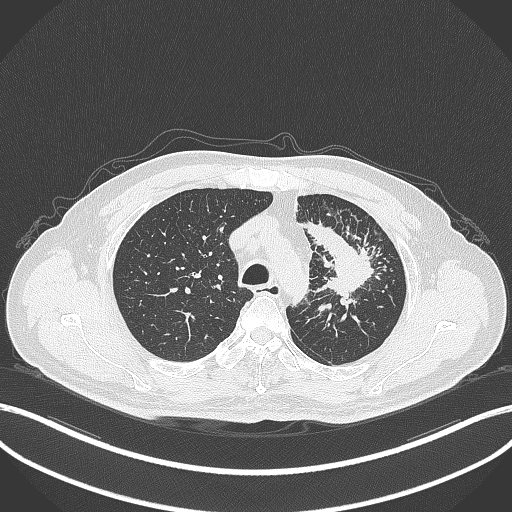
Chest CT, one axial slice. Slice 273 of 386 in the series (ordered by position). 120 kVp. Lung window (W 1500 / L -600 HU). 1 mm slice thickness. 512 × 512 image matrix. Patient: male, 69 years. Case-level facts recorded for this patient, not image findings: clinical TNM (as recorded): T2a N2 M0; histopathological grade: G2-3.
Outlined on this slice (rectangle marked by the reading radiologist):
- lung tumour (recorded histology: adenocarcinoma): bounding box <303,218,380,307> (left, top, right, bottom; pixels)